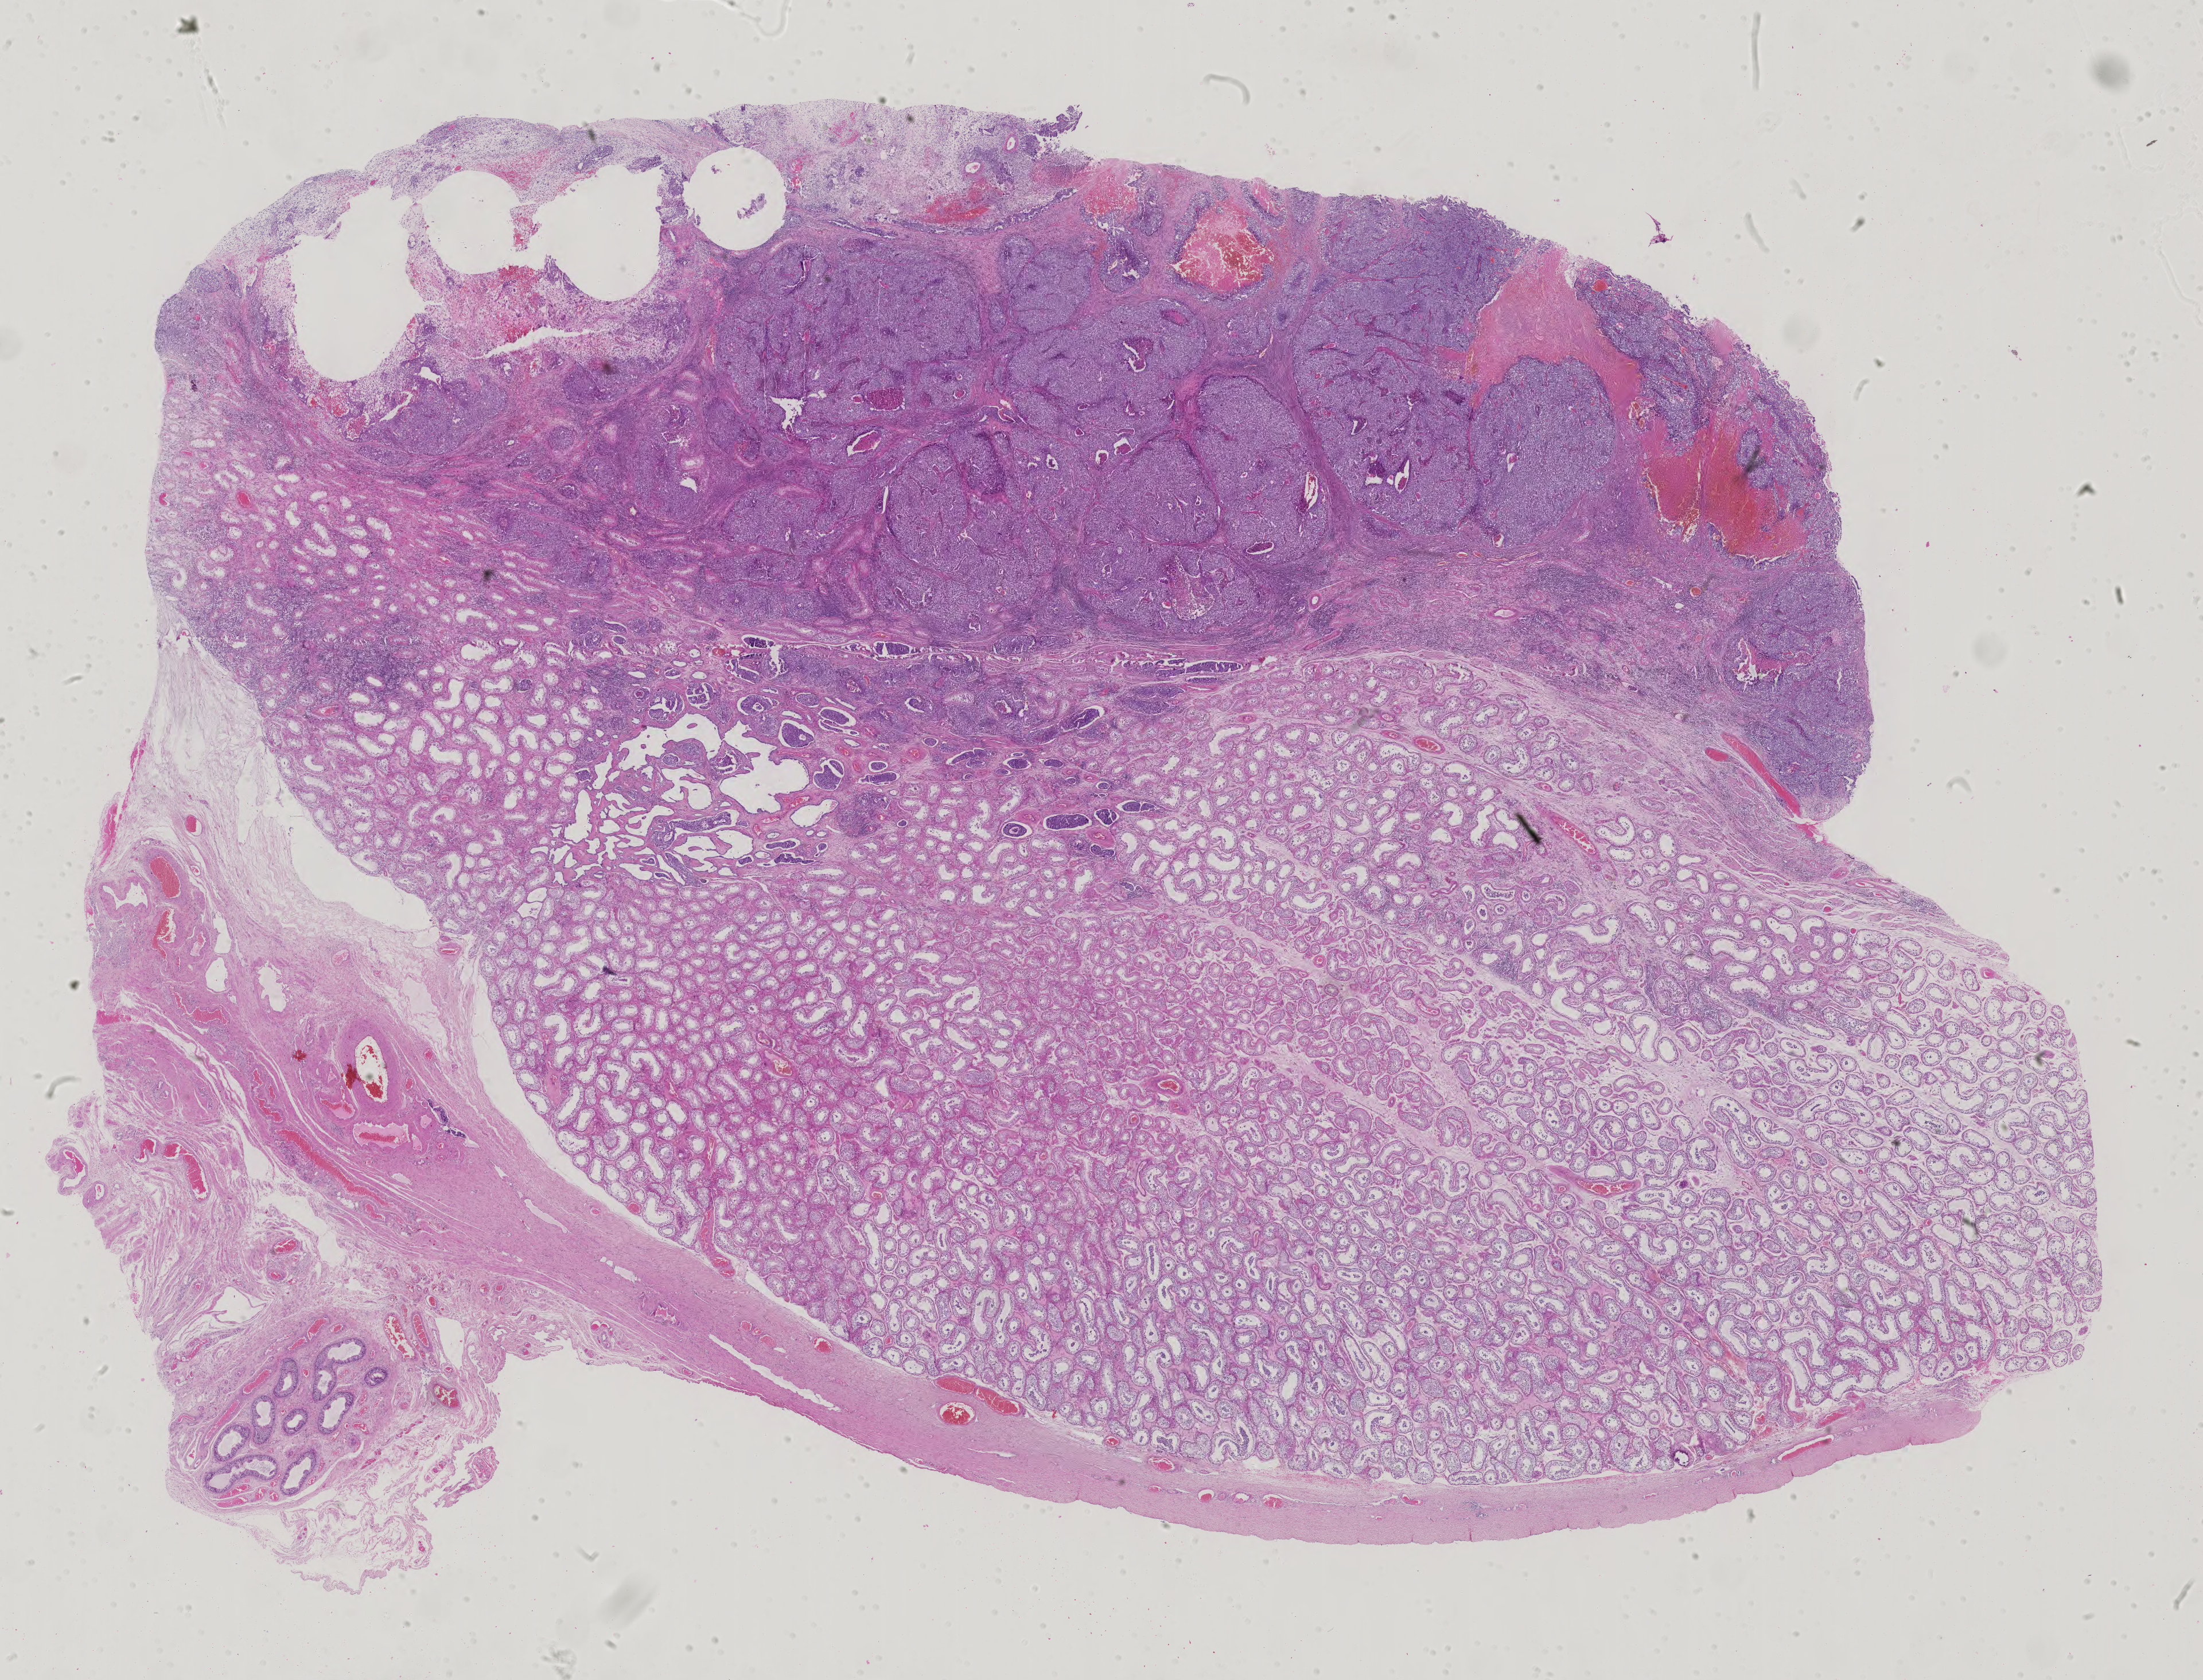
Whole-slide histology image, H&E — whole scanned area (about 28.0 x 21.3 mm, acquisition: 40x scan) shown as a low-resolution overview; FFPE section; sample: primary tumour, testis. Male patient; age at initial diagnosis 41 years.
Laterality: left. TNM: T2 N1 M0. Histologic diagnosis: Embryonal carcinoma, NOS. AJCC pathologic stage: IIIB (6th edition).